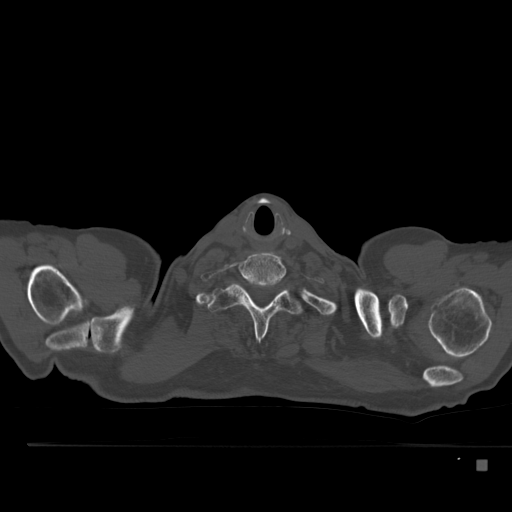
CT including the spine, one axial slice; position 430 of 517 along the scan axis; 120 kVp; bone window (W 1800 / L 400 HU); 1.5 mm slice thickness; 512 × 512 image matrix, field of view 408 × 408 mm. Patient: male, 70 years. Case-level facts recorded for this patient, not image findings: primary cancer: renal.
Annotated regions visible in this slice (semi-automatically segmented with operator editing):
- T1 vertebra: box from (x=207, y=284) to (x=300, y=341) px